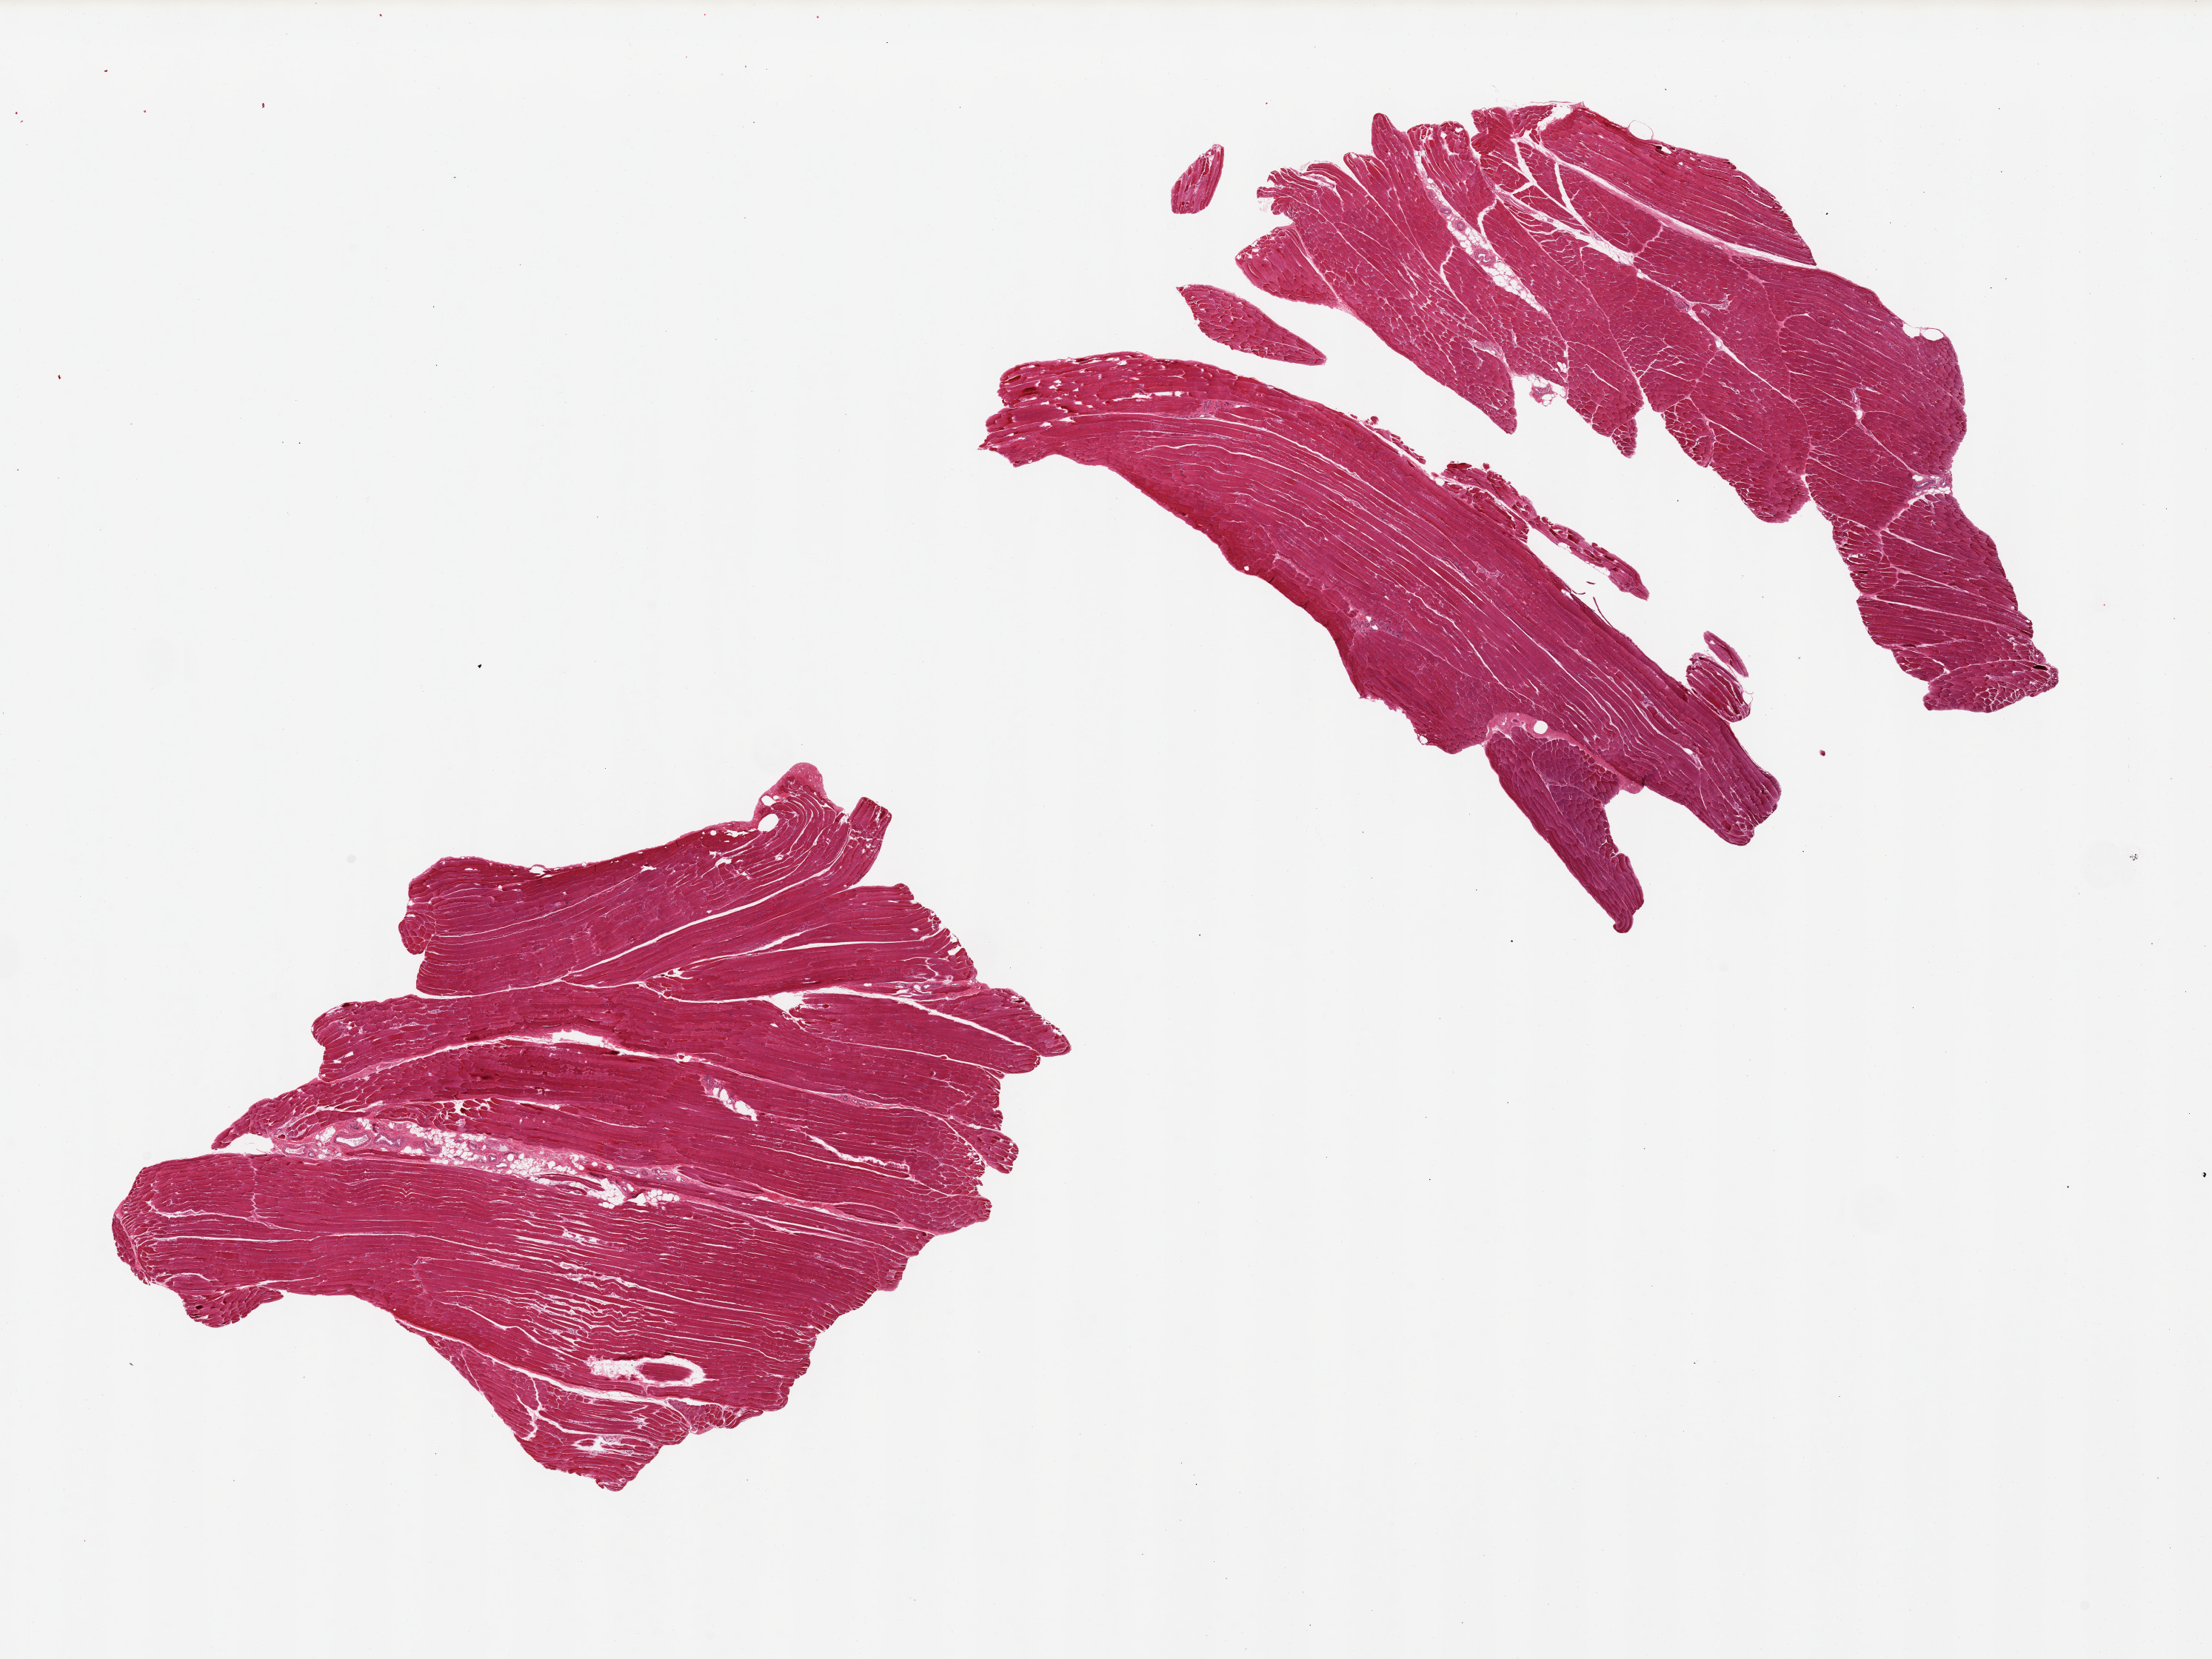
Digitized haematoxylin and eosin-stained section, a low-resolution overview of the entire scanned area, about 23.6 x 17.7 mm (acquisition: 20x scan). PAXgene-fixed paraffin-embedded (PFPE) section. Section of skeletal muscle (target tissue). Tissue donor sample. Donor: male.
Pathologist's review note for this sample: 2 pieces.